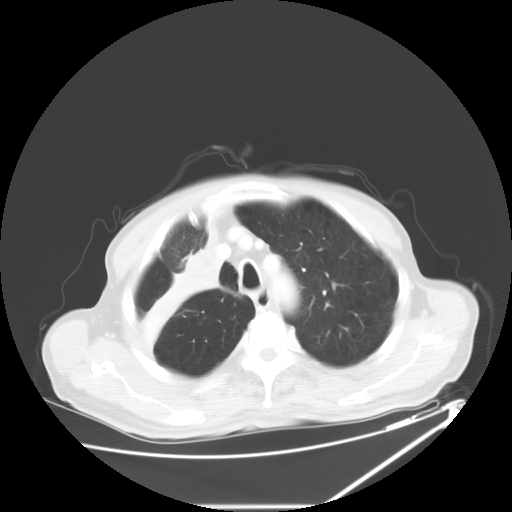
Chest CT, one axial slice. Slice 49 of 60 in the series (ordered by position). 120 kVp. Lung window (W 1500 / L -600 HU). 512 × 512 image matrix, field of view 410 × 410 mm. Male patient, age 73 years. From the clinical record (not read from this slice): clinical TNM (as recorded): T2a N1 M0.
Outlined on this slice (rectangle marked by the reading radiologist):
- lung tumour (recorded histology: squamous cell carcinoma): bounding box <134,221,224,353> (left, top, right, bottom; pixels)